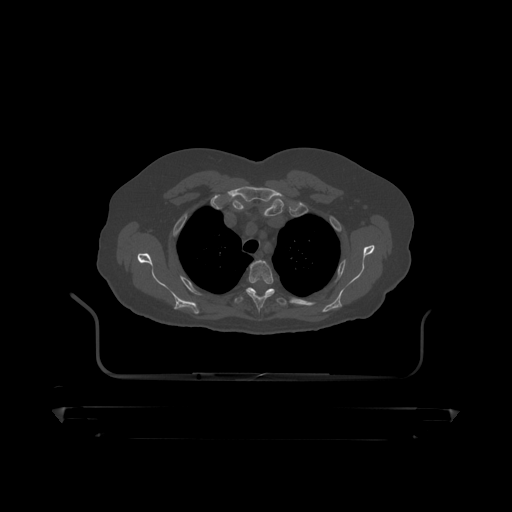
CT including the spine, one axial slice. Position 353 of 390 along the scan axis. Bone window (W 1800 / L 400 HU). 1.25 mm slice thickness. 512 × 512 image matrix, field of view 650 × 650 mm. Patient: male, 60 years. From the clinical record (not read from this slice): primary cancer: prostate.
Outlined on this slice (semi-automatically segmented with operator editing):
- T3 vertebra: bounding box (x1, y1, x2, y2) in pixels: (247, 261, 274, 310)
- T4 vertebra: (234, 288, 287, 307)